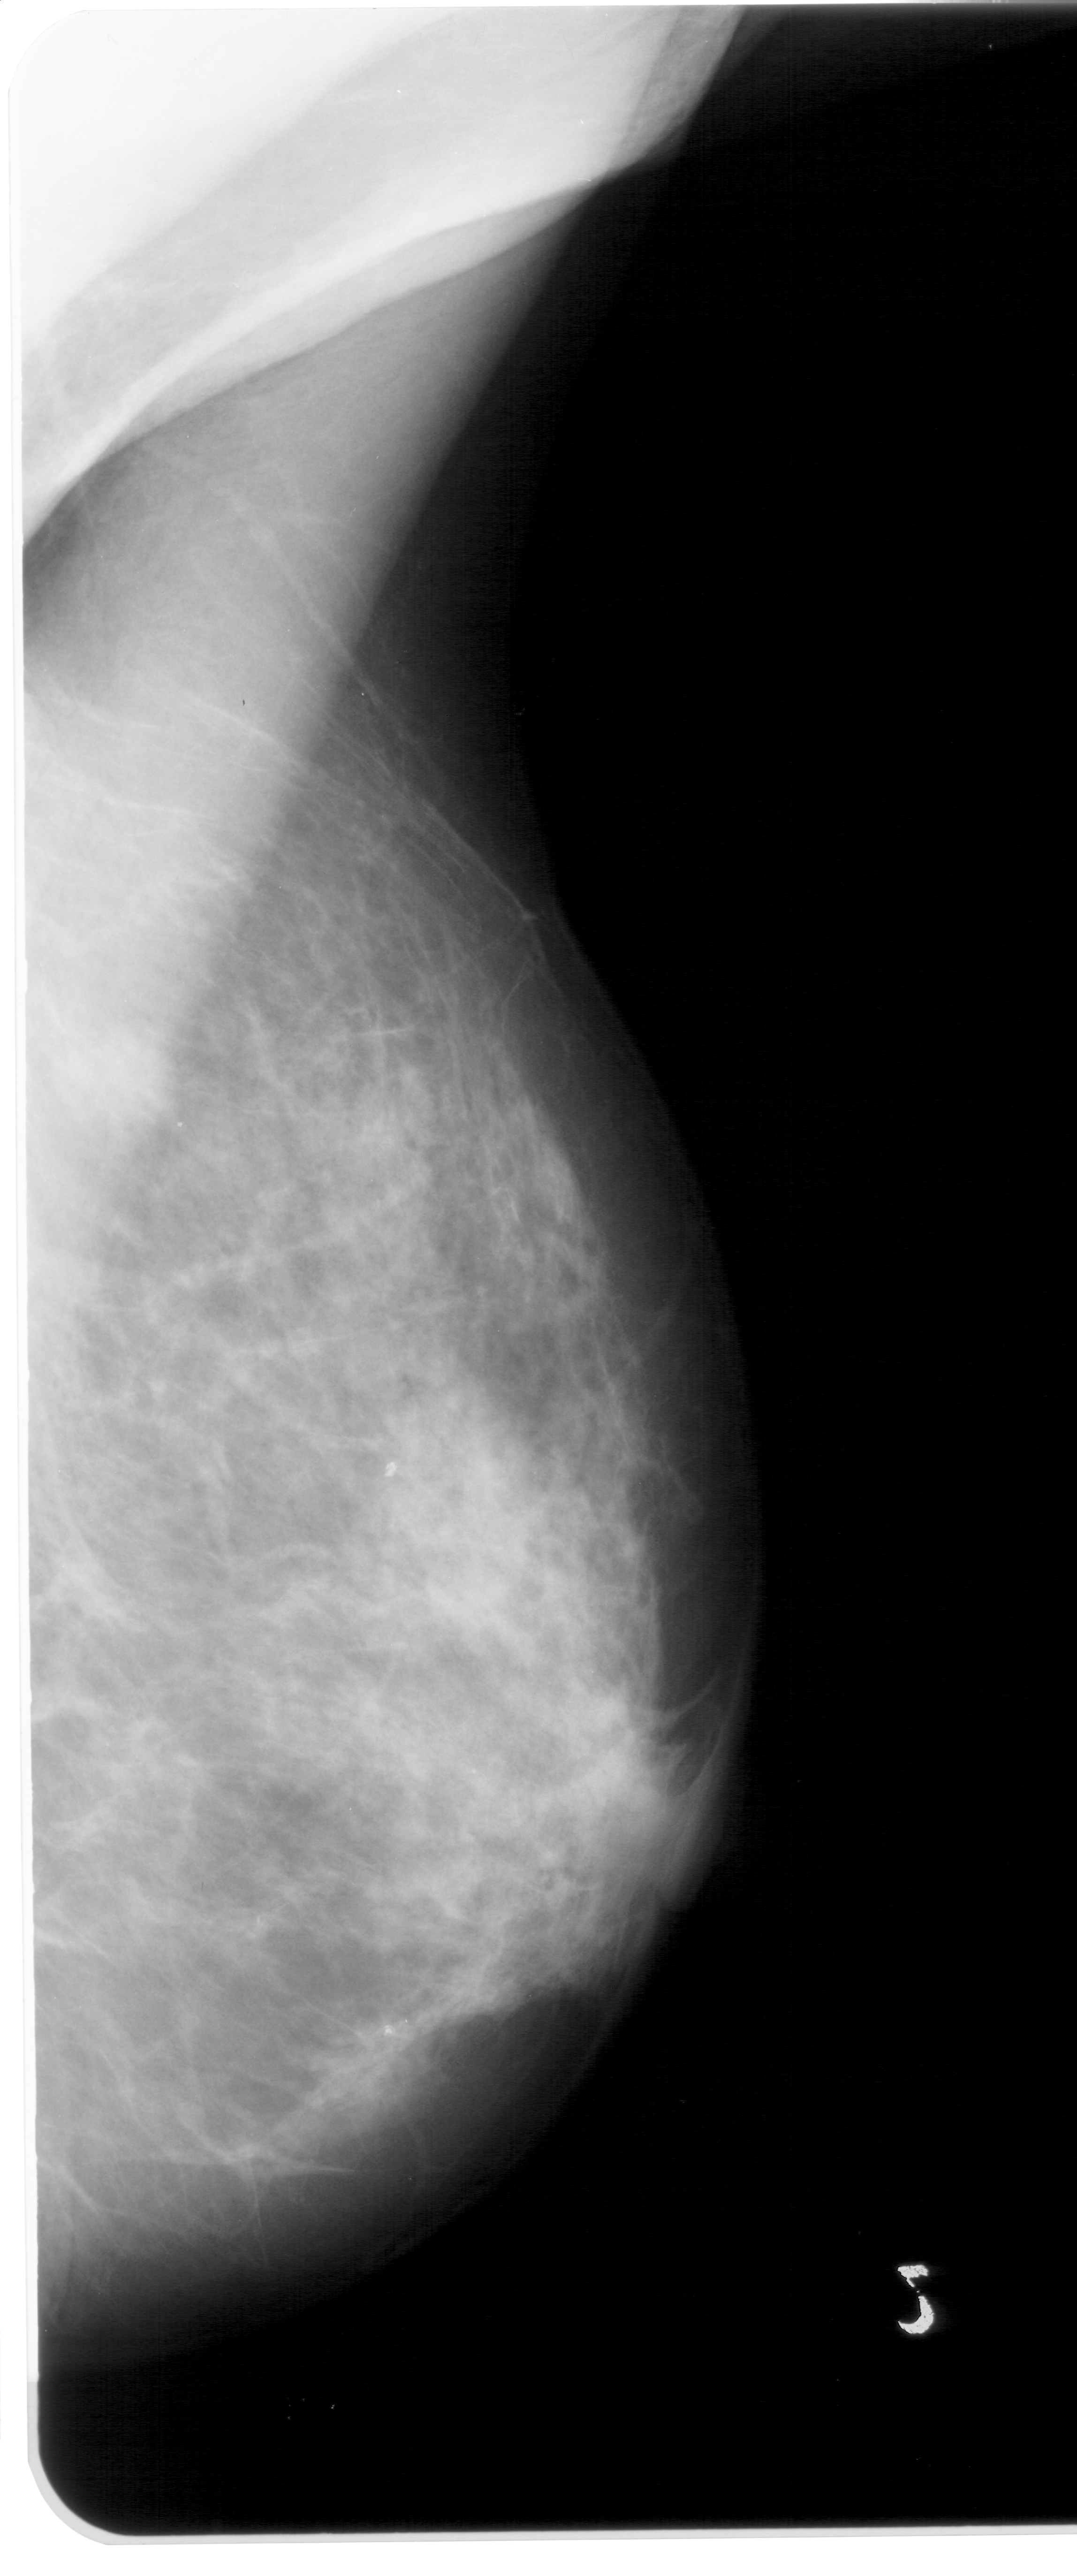
Mammogram (digitized film); right breast; MLO view; breast composition: extremely dense (BI-RADS density category 4 of 4).
Abnormality record for this image: mass, shape irregular, margins ill defined; BI-RADS assessment category 4; pathology (as recorded): benign.